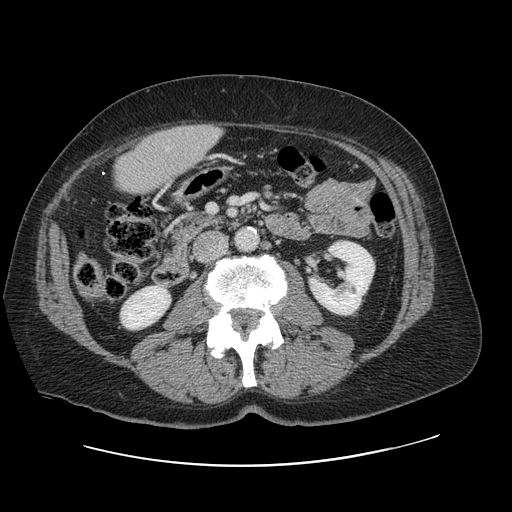
Contrast-enhanced abdominal CT, one axial slice; position 20 of 138 along the scan axis; 120 kVp; soft-tissue window (W 400 / L 40 HU); 2.5 mm slice thickness; 512 × 512 image matrix, field of view 402 × 402 mm. Male patient, age 71 years. Case-level facts recorded for this patient, not image findings: diagnosis: colorectal cancer liver metastases, imaged before liver resection; multiple liver metastases: no; largest metastasis: 3.3 cm.
Structures marked on this image (expert manual segmentation):
- liver: bounding box (x1, y1, x2, y2) in pixels: (116, 125, 221, 194)
- planned liver remnant (the part of the liver to remain after resection): (114, 136, 176, 194)